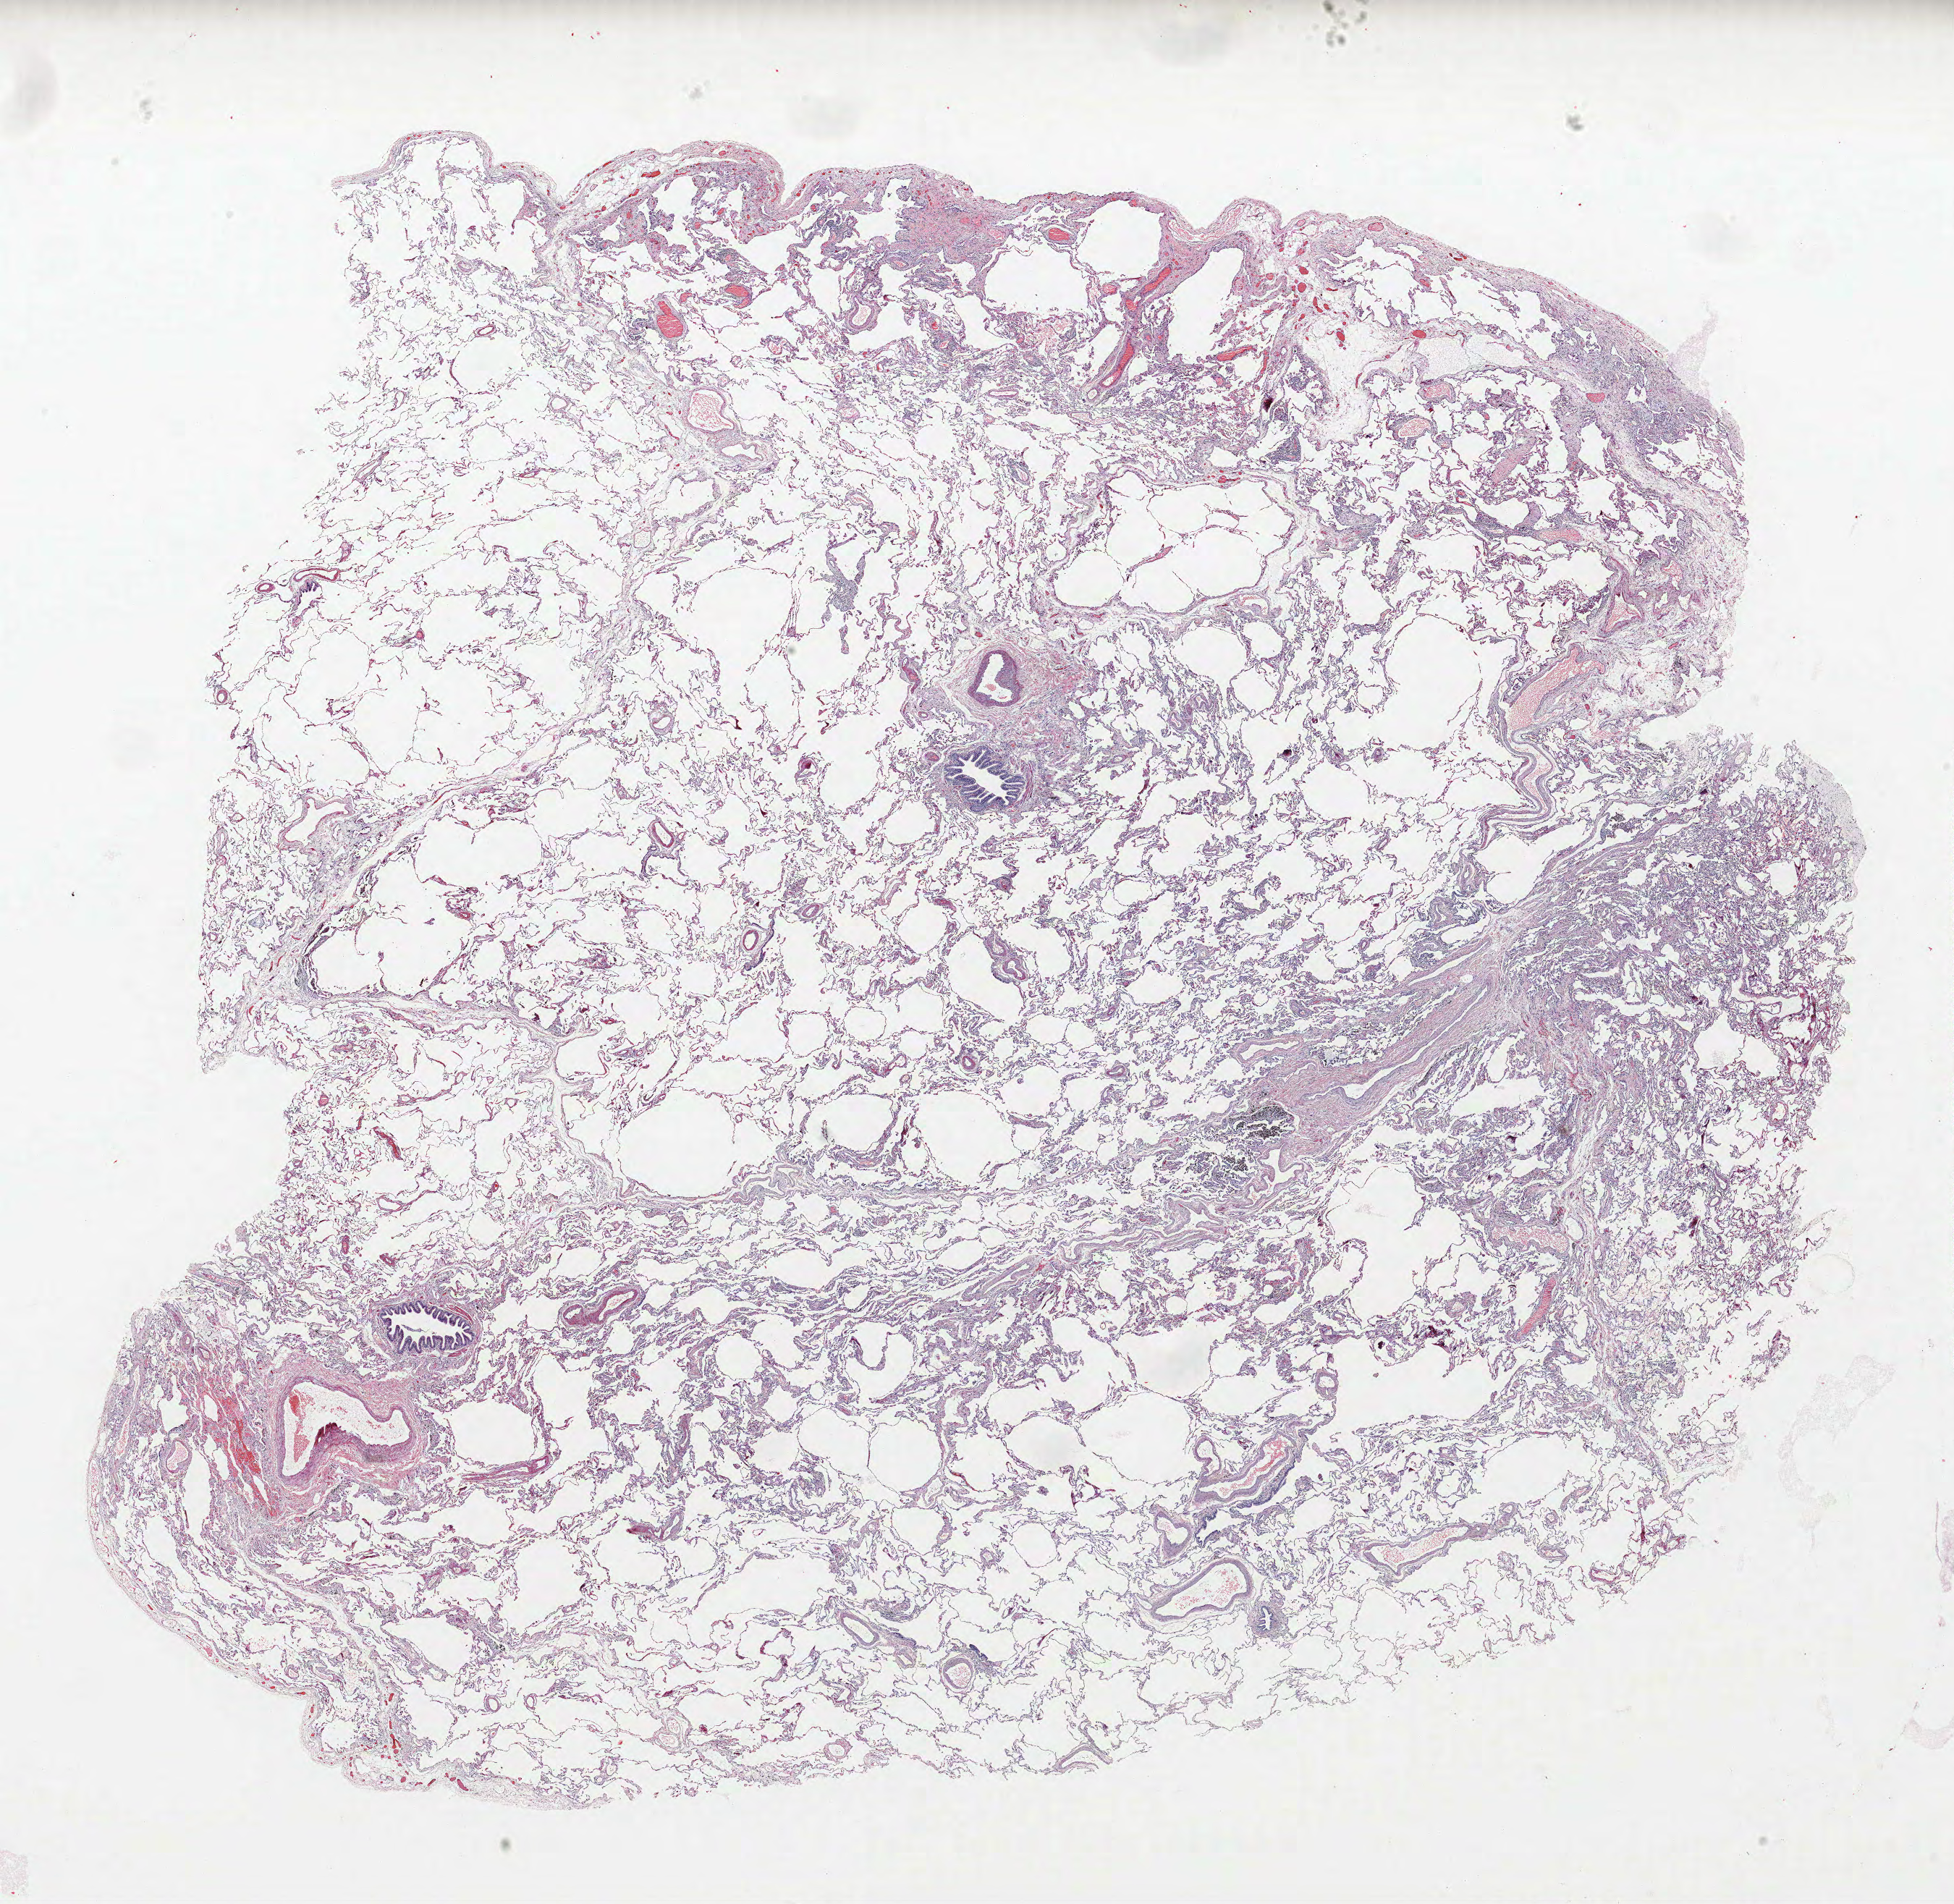
H&E whole-slide image, whole scanned area (about 21.6 x 21.1 mm, slide scanned at 40x) shown as a low-resolution overview, FFPE section, lung tissue. Male patient, aged 65 at enrolment. Current smoker at enrolment. Grade: poorly differentiated (G3).
Primary tumour location (clinical record): right lower lobe. Participant's lung-cancer diagnosis: Adenocarcinoma, NOS (ICD-O-3 8140/3). Tumour size (pathology): 25 mm. ICD-O-3 topography: lower lobe of lung (C34.3). Stage (AJCC 6th edition): IIIA.